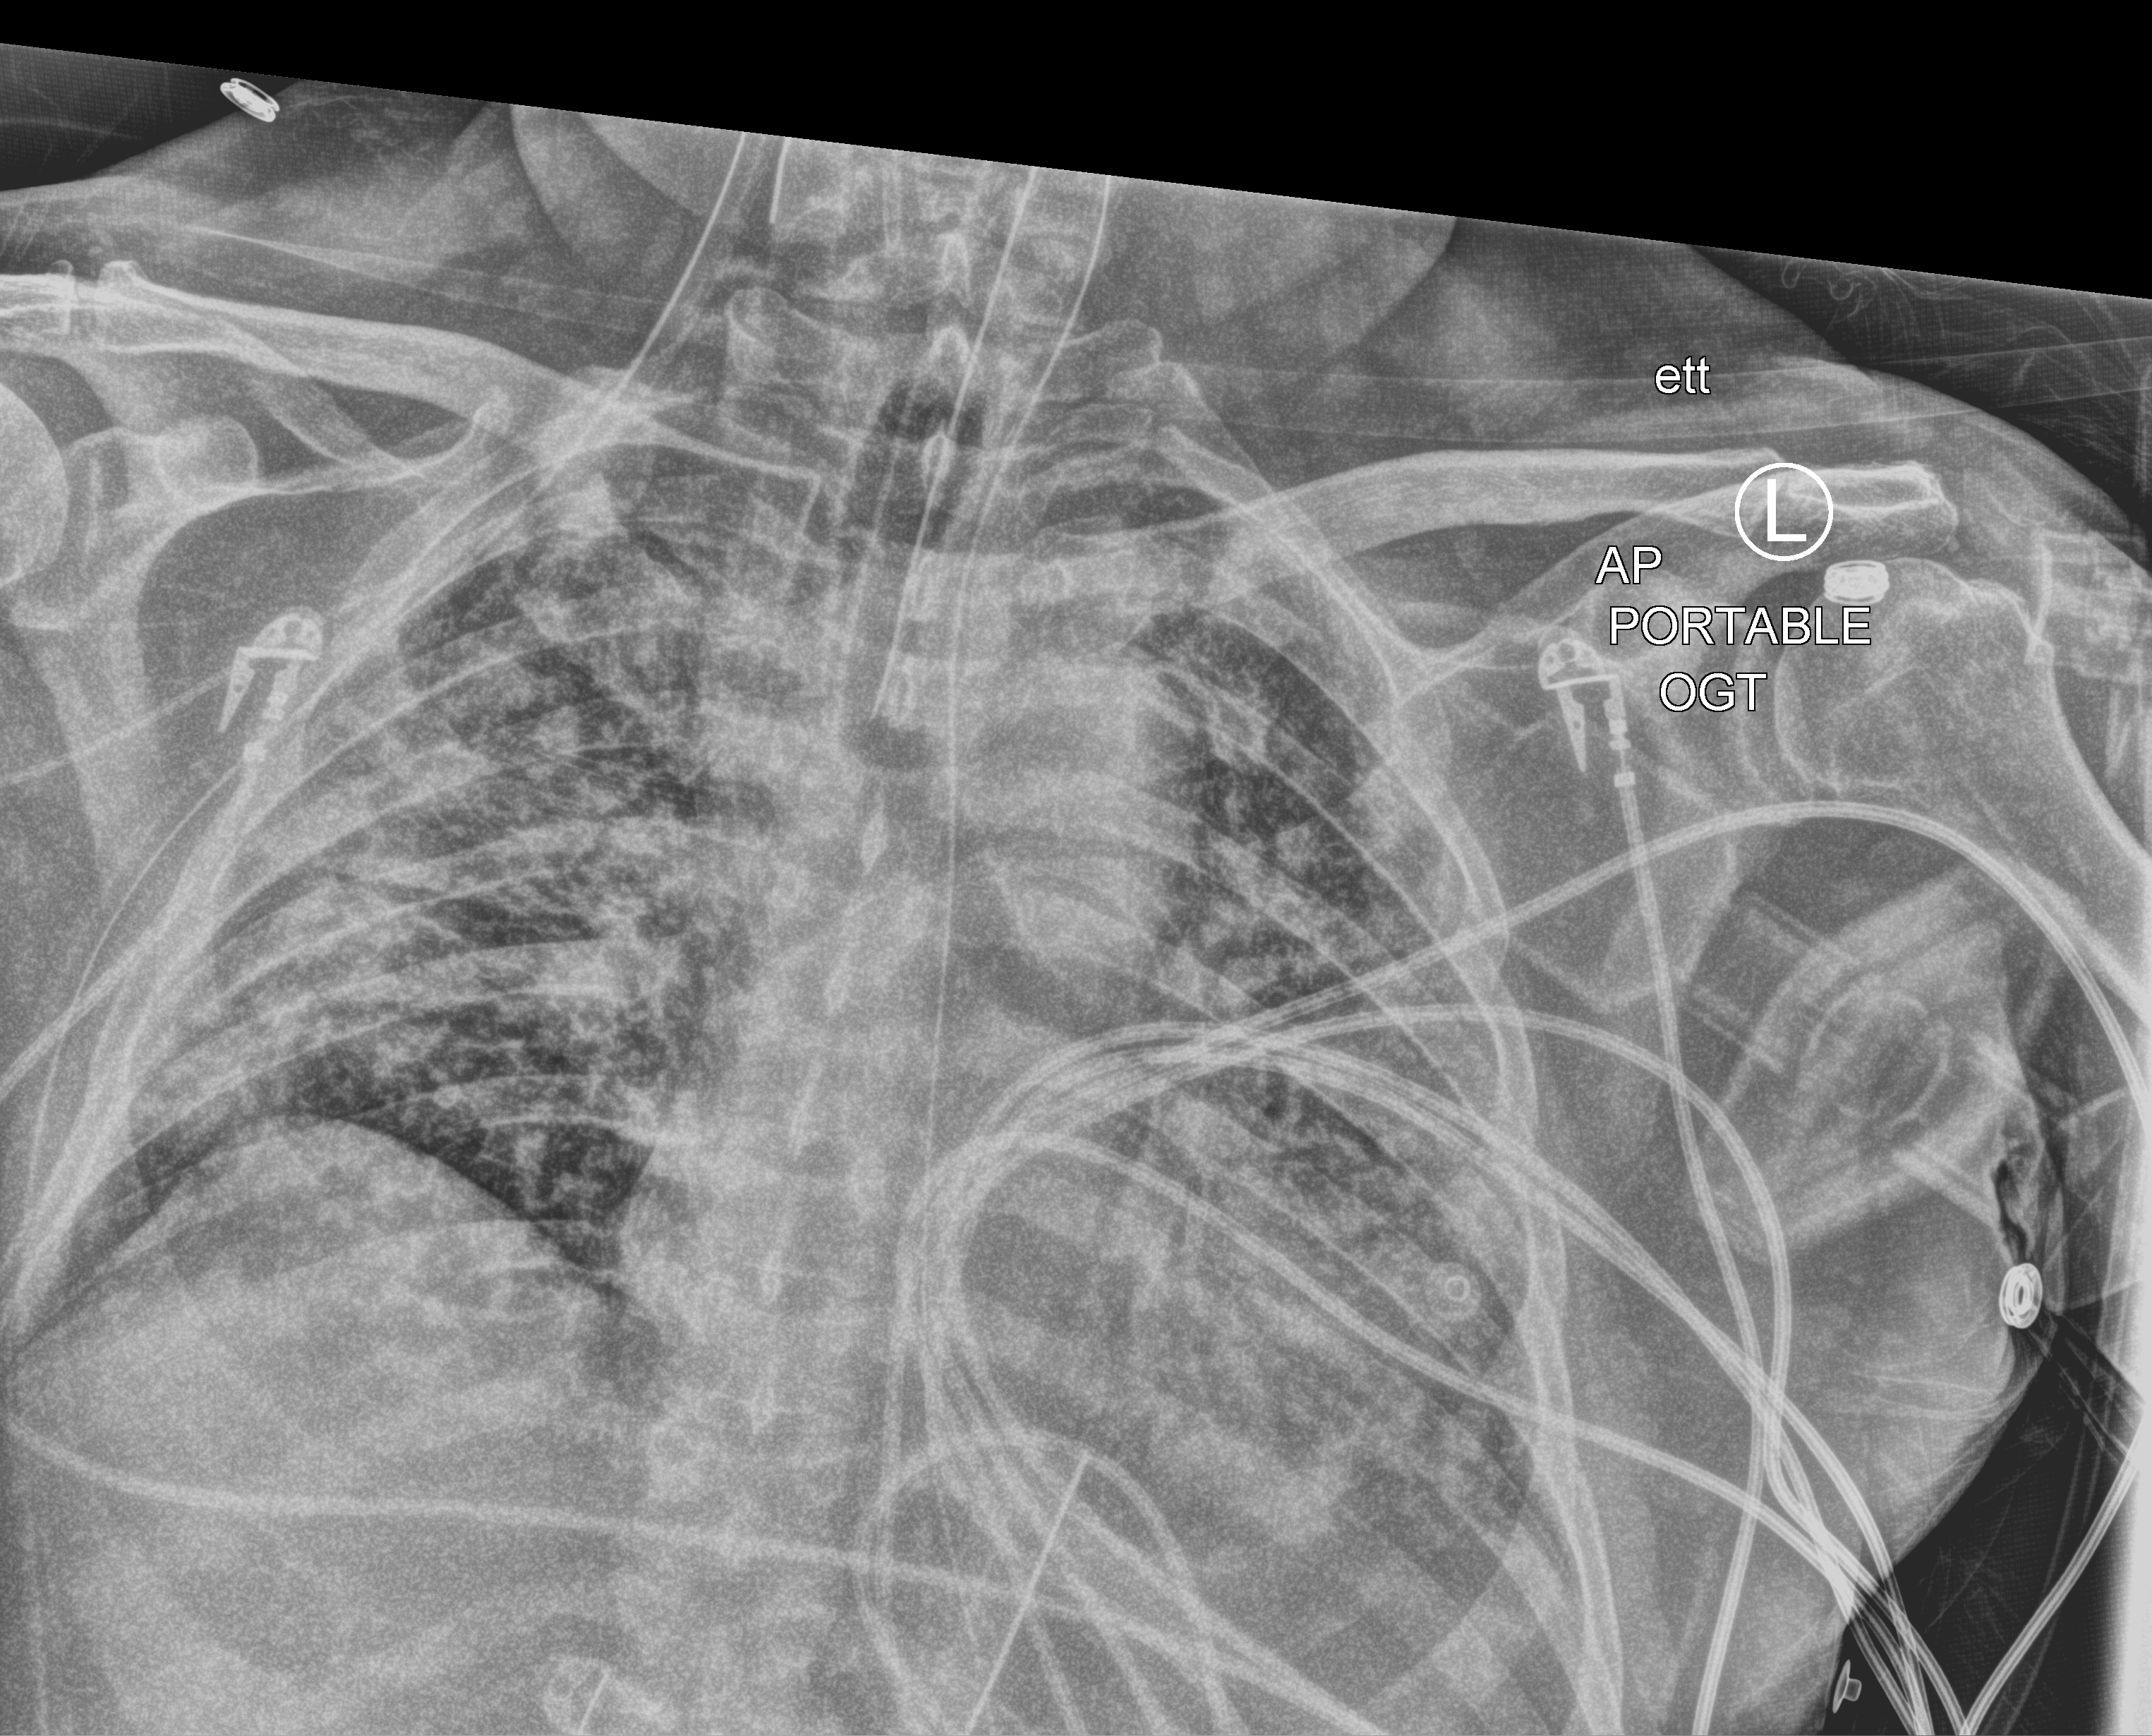
Bedside chest radiograph (computed radiography), anteroposterior (AP) projection. Patient hospitalised with COVID-19; male, aged 60–74 years.
Hospital-stay facts (about this admission, not read from this image; timing relative to this image not recorded):
- mechanically ventilated during this hospital stay: yes
- admitted to intensive care during this hospital stay: yes
- smoking status (admission record): former